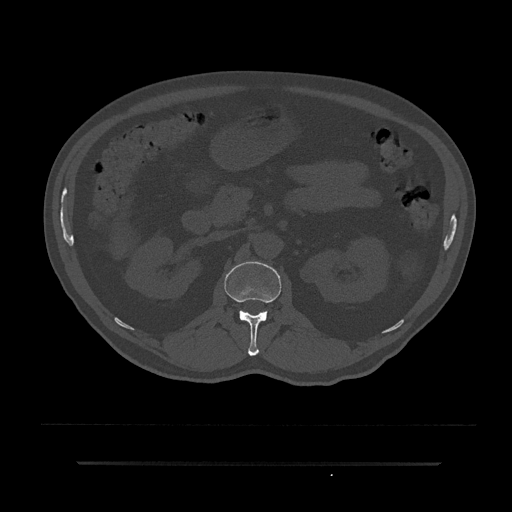
CT including the spine, one axial slice; slice 131 of 797 in the series (ordered by position); reconstruction kernel Br40s/3; 120 kVp; bone window (W 1800 / L 400 HU); 0.5 mm slice thickness; 512 × 512 image matrix. Male patient, age 59 years. From the clinical record (not read from this slice): primary cancer: bile ducts.
Annotated regions visible in this slice (semi-automatically segmented with operator editing):
- L1 vertebra: bounding box <224,261,281,356> (left, top, right, bottom; pixels)